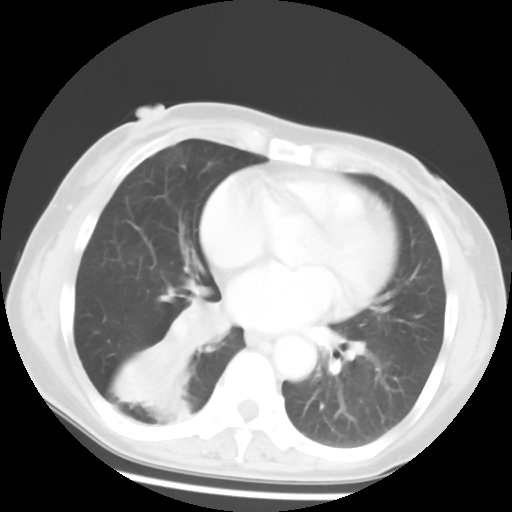
Chest CT, one axial slice. Slice 24 of 52 in the series (ordered by position). Reconstruction kernel STANDARD. Lung window (W 1500 / L -600 HU). 5 mm slice thickness. 512 × 512 image matrix. Patient: female, 54 years. From the clinical record (not read from this slice): clinical TNM (as recorded): T1c N0 M0.
Structures marked on this image (bounding box drawn by a radiologist):
- lung tumour (recorded histology: squamous cell carcinoma): bounding box <175,283,242,363> (left, top, right, bottom; pixels)